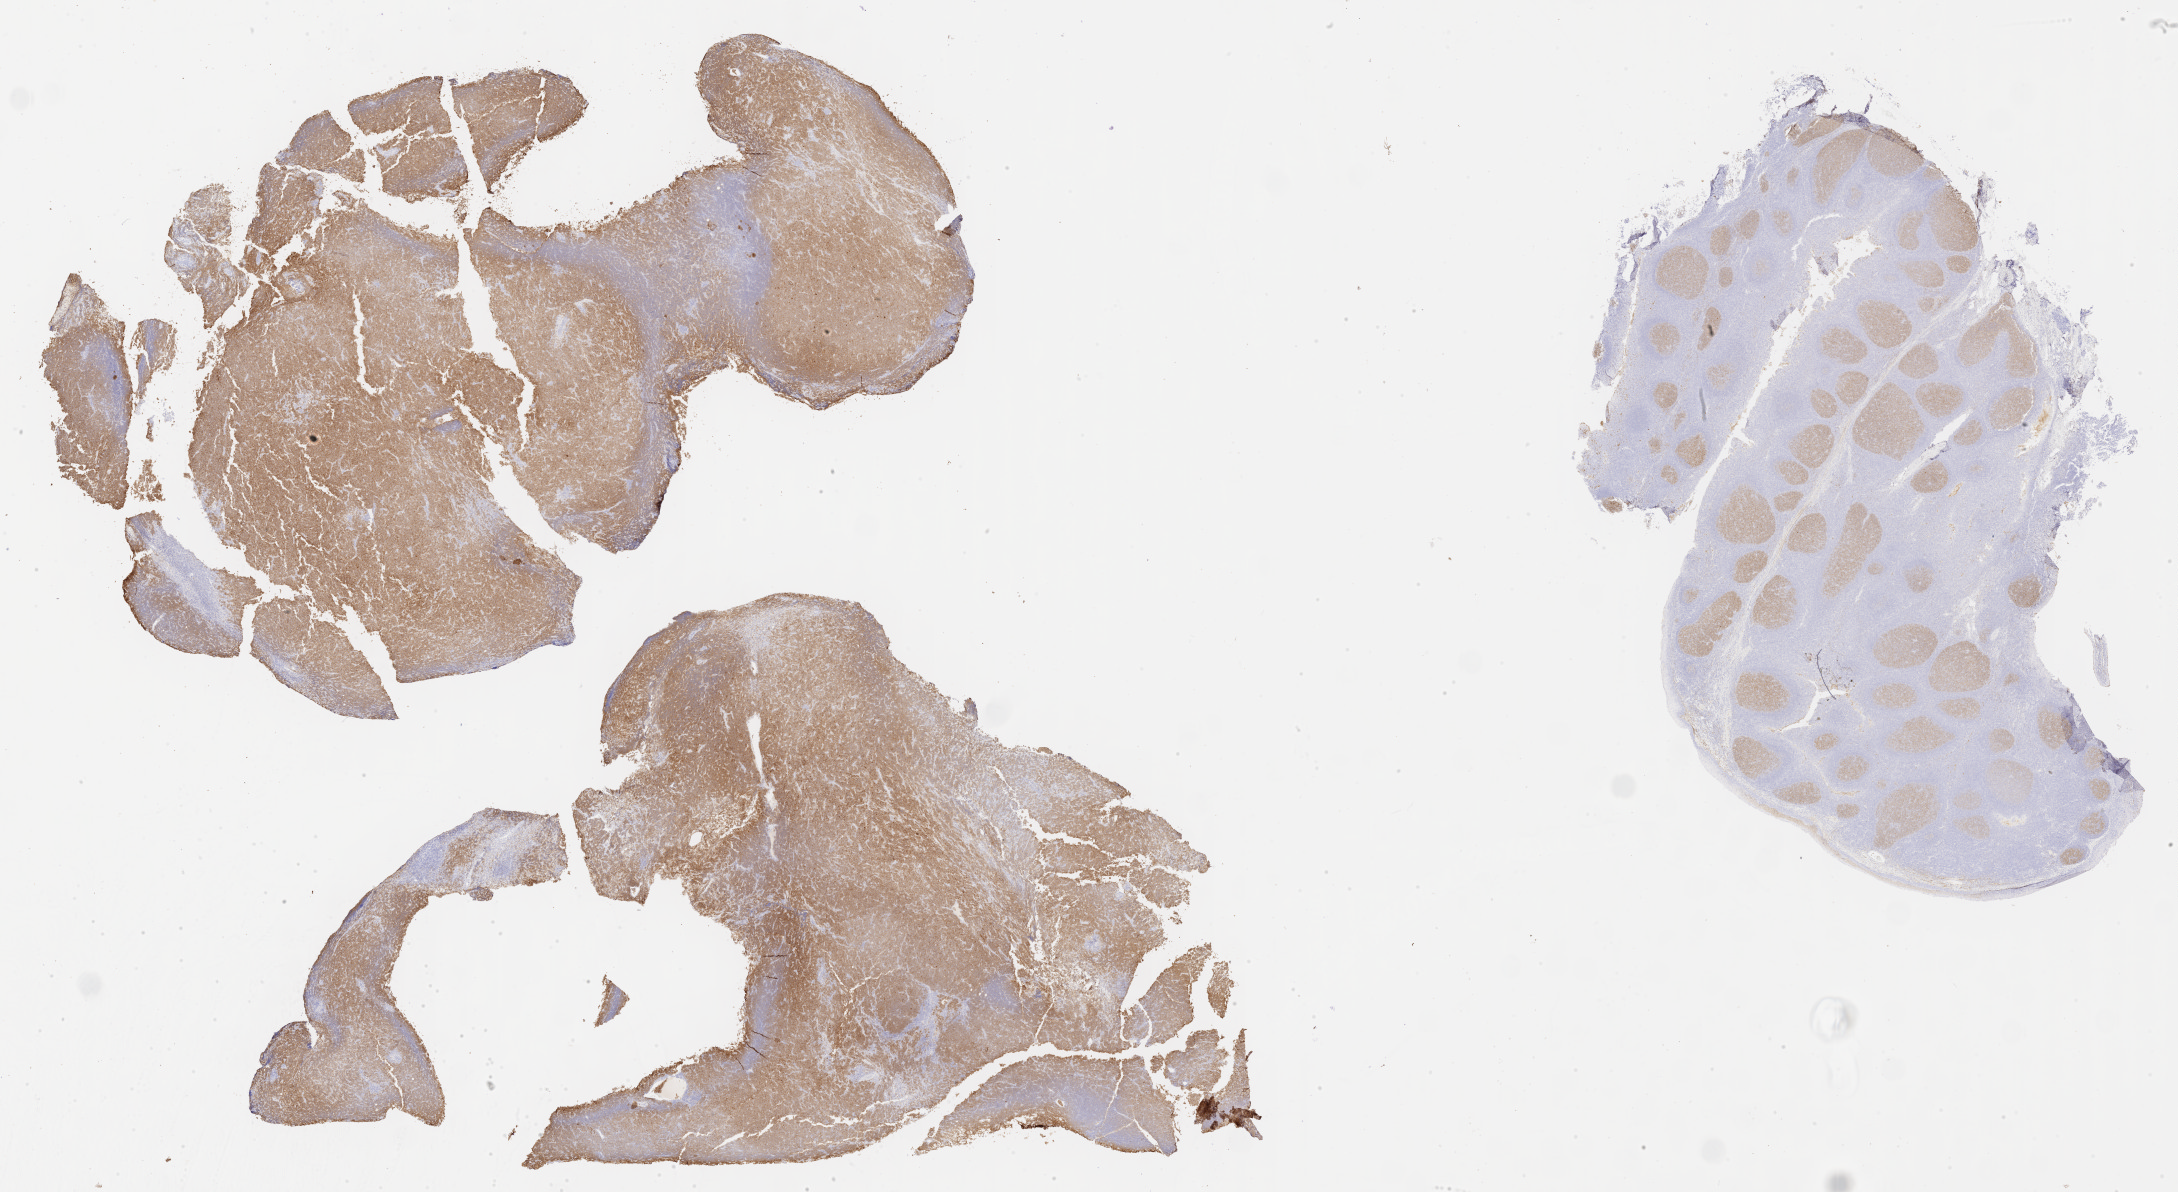
IHC for CD10, whole-slide image — shown as a low-resolution overview of the whole scanned area (about 35.2 x 19.3 mm), tumor tissue, site: liver. Male patient, age 45 years.
Histologic diagnosis: Diffuse large B-cell lymphoma, NOS.